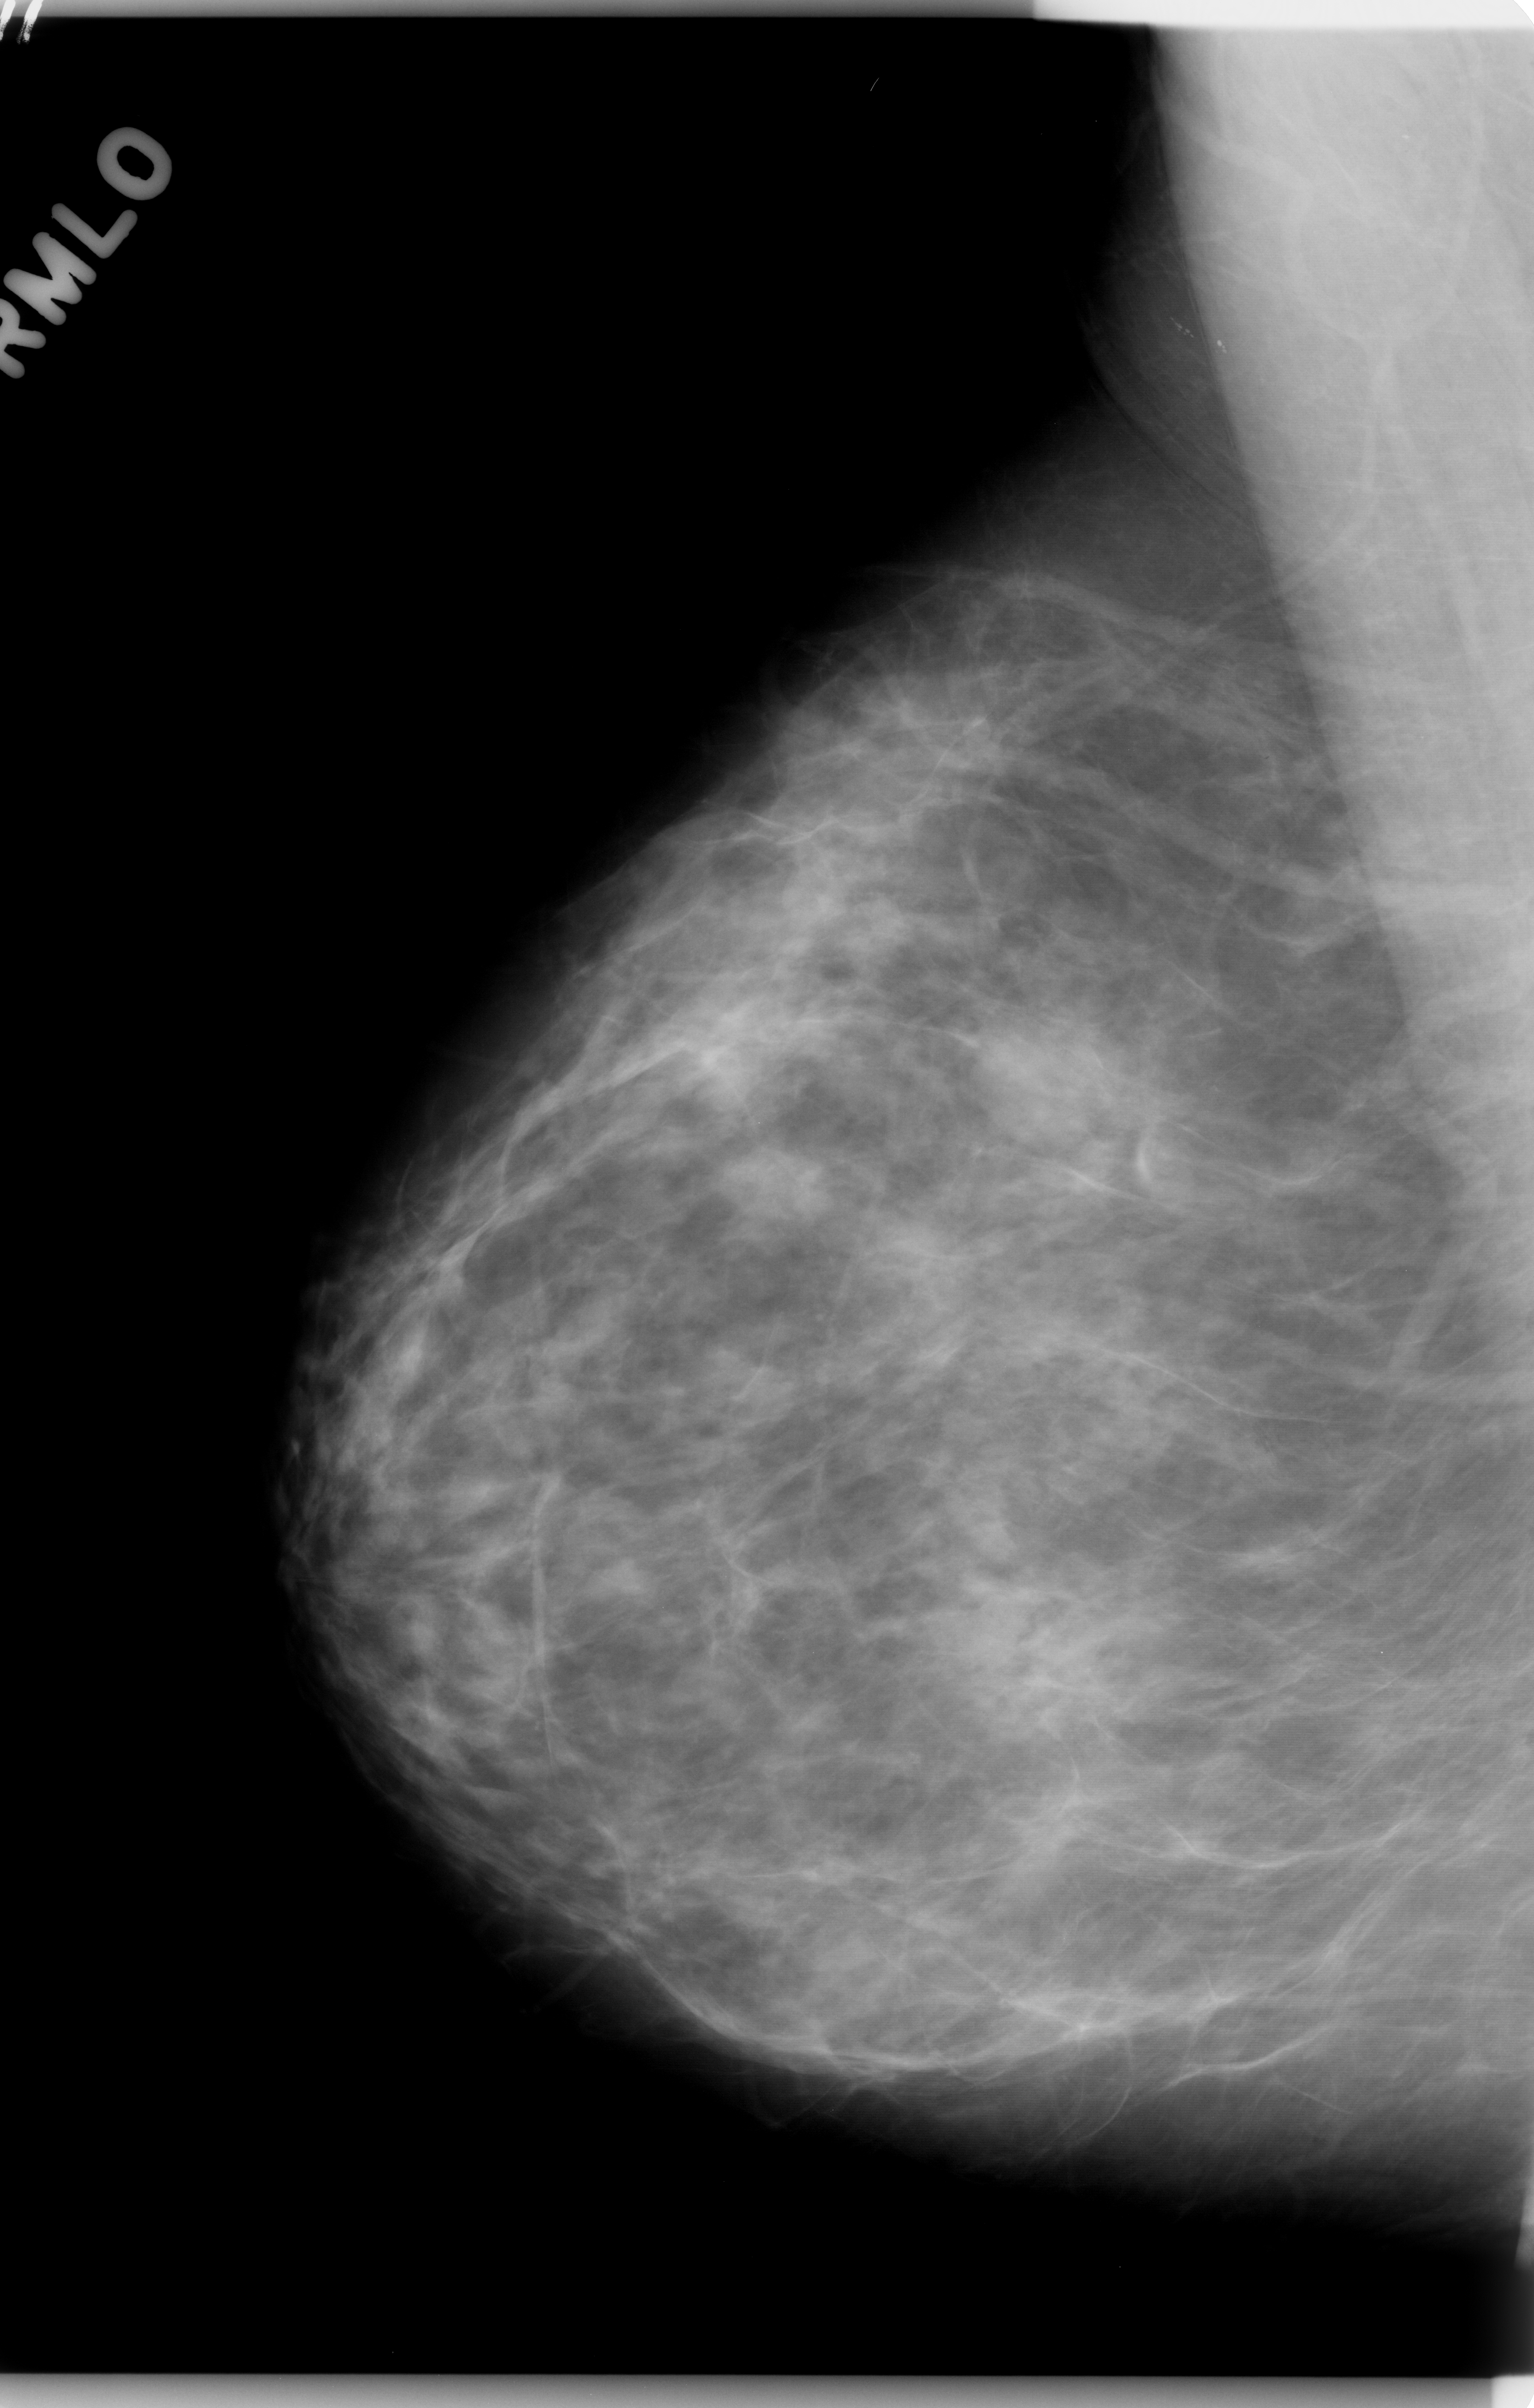
Mammogram (digitized film). Right breast. Mediolateral oblique (MLO) view. BI-RADS breast density category 2 (scale 1–4). 1534 × 2408 image matrix.
Expert-marked regions of interest on this image (one box per marked abnormality):
- mass, shape oval, margins circumscribed; BI-RADS assessment category 4; subtlety rating 4 on a 1 (subtle) to 5 (obvious) scale; pathology result (as recorded, not read from the image): benign: bounding box (x1, y1, x2, y2) in pixels: (958, 991, 1126, 1144)